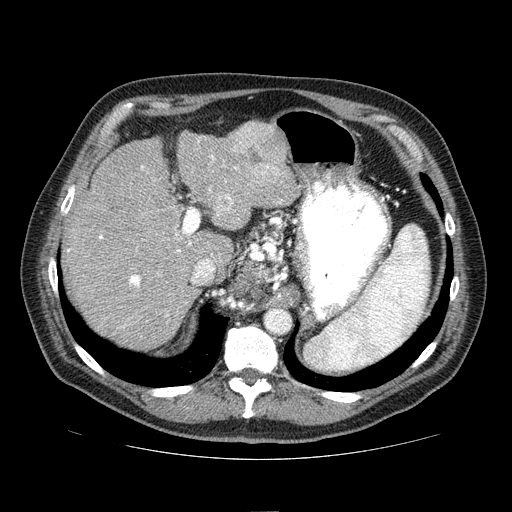
Contrast-enhanced abdominal CT (liver protocol), one axial slice. Position 52 of 81 along the scan axis. Reconstruction kernel STANDARD. One of 2 acquisitions stored at this slice position. Soft-tissue window (W 400 / L 40 HU). 2.5 mm slice thickness. 512 × 512 image matrix, field of view 400 × 400 mm. Case-level facts recorded for this patient, not image findings: diagnosis: hepatocellular carcinoma (patient treated with transarterial chemoembolisation; whether this scan precedes or follows treatment is not stated here); TNM stage (as recorded): Stage-IIIA.
Annotated regions visible in this slice (semi-automatically segmented with operator editing):
- liver parenchyma outside the tumour (the mass and vessels are separate outlines, so this box may not span the whole liver): bounding box (x1, y1, x2, y2) in pixels: (62, 120, 298, 348)
- mass: (219, 121, 288, 188)
- liver vessels: (67, 139, 282, 328)